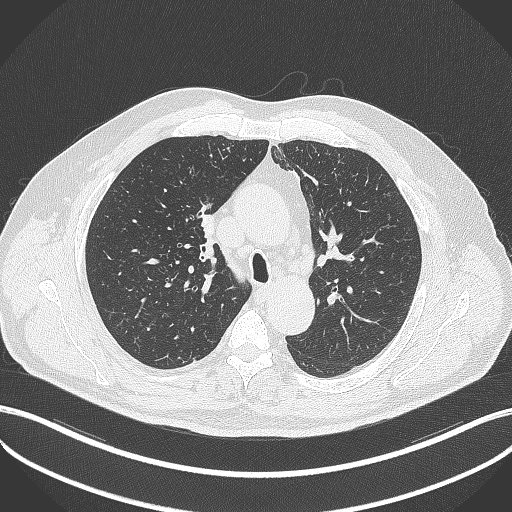
Chest CT, one axial slice. Position 262 of 411 along the scan axis. Lung window (W 1500 / L -600 HU). 1 mm slice thickness. 512 × 512 image matrix, field of view 400 × 400 mm. Male patient, age 60 years. Case-level facts recorded for this patient, not image findings: clinical TNM (as recorded): T1b N1 M0.
Outlined on this slice (rectangle marked by the reading radiologist):
- lung tumour (recorded histology: squamous cell carcinoma): bounding box (x1, y1, x2, y2) in pixels: (197, 209, 221, 249)